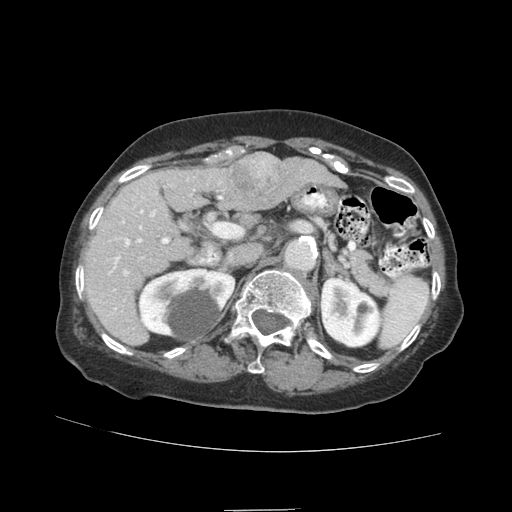
Contrast-enhanced abdominal CT (liver protocol), one axial slice; slice 51 of 89 in the series (ordered by position); reconstruction kernel STANDARD; soft-tissue window (W 400 / L 40 HU); 2.5 mm slice thickness; 512 × 512 image matrix, field of view 360 × 360 mm. From the clinical record (not read from this slice): diagnosis: hepatocellular carcinoma (patient treated with transarterial chemoembolisation; whether this scan precedes or follows treatment is not stated here); TNM stage (as recorded): Stage-II; Child-Pugh class: A; tumour differentiation: moderately differentiated; tumour nodularity: multinodular.
Annotated regions visible in this slice (semi-automatically segmented with operator editing):
- liver parenchyma outside the tumour (the mass and vessels are separate outlines, so this box may not span the whole liver): bounding box (x1, y1, x2, y2) in pixels: (84, 152, 338, 344)
- mass: (227, 152, 290, 209)
- liver vessels: (108, 178, 222, 314)